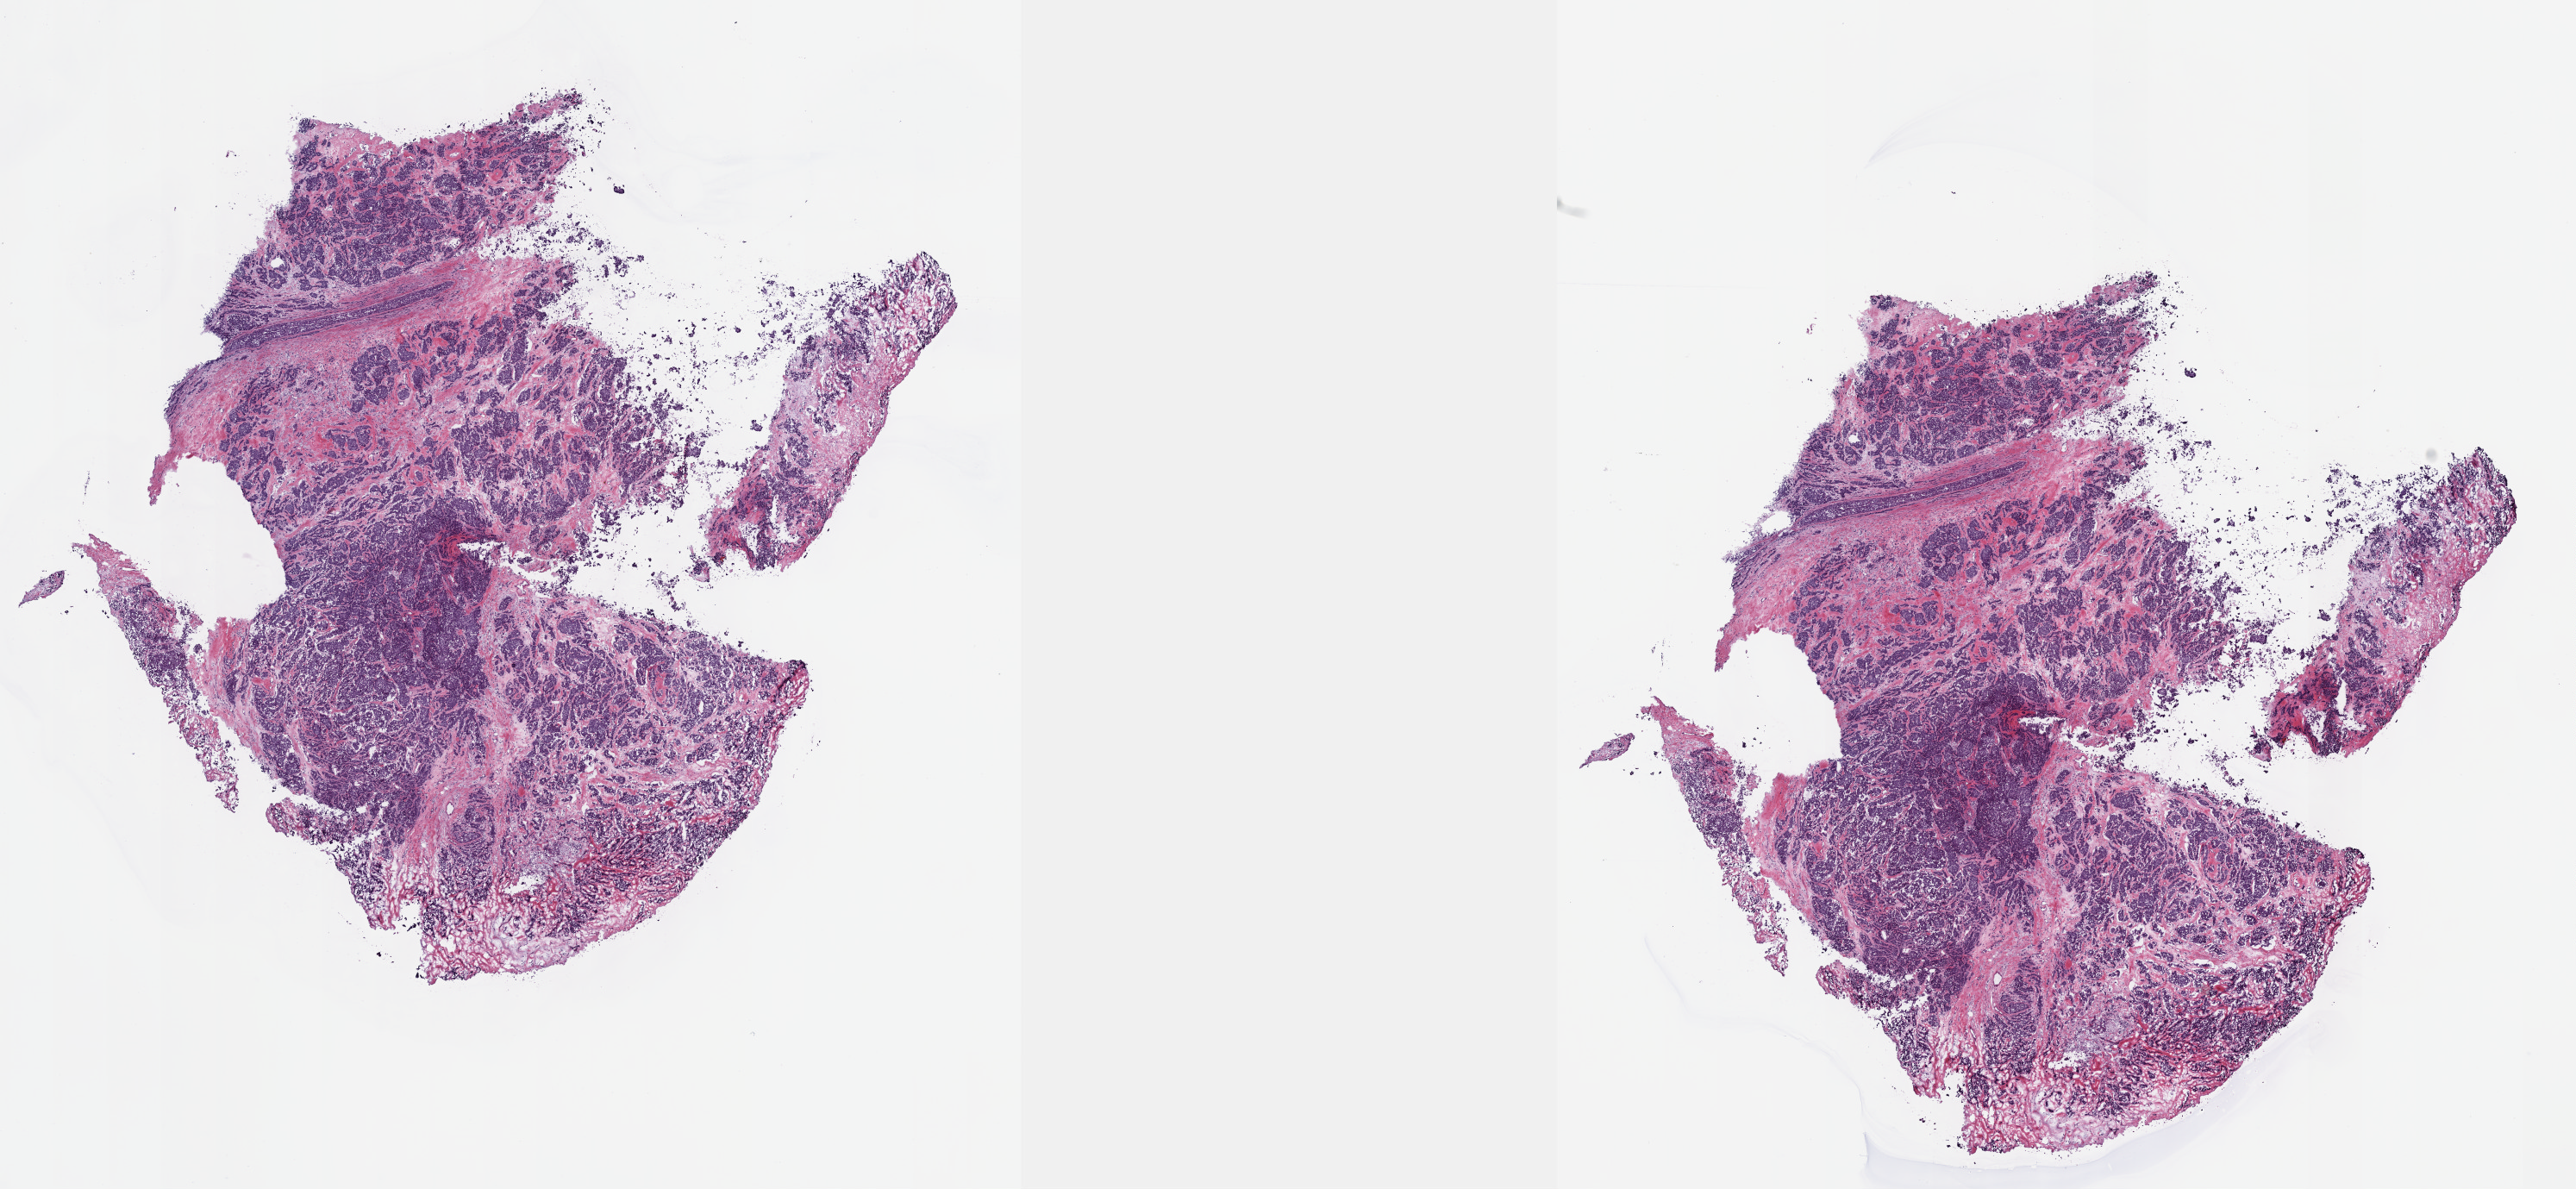
Digitized H&E tissue section (whole slide), shown as a low-resolution overview of the whole scanned area (about 24.1 x 11.1 mm, acquisition: 40x scan). Frozen section. Breast, primary tumour sample. Patient: female, age at initial diagnosis 73 years. Pathologist review of this section (percent, as recorded): tumour cells 70%, tumour nuclei 70%, normal cells 5%, stromal cells 25%, necrosis 0%. Infiltration values recorded for this section: lymphocyte infiltration 5%, monocyte infiltration 0%, neutrophil infiltration 0%.
TNM: T2 N0 MX. Diagnosis: Infiltrating duct carcinoma, NOS. AJCC pathologic stage: IIA (7th edition).